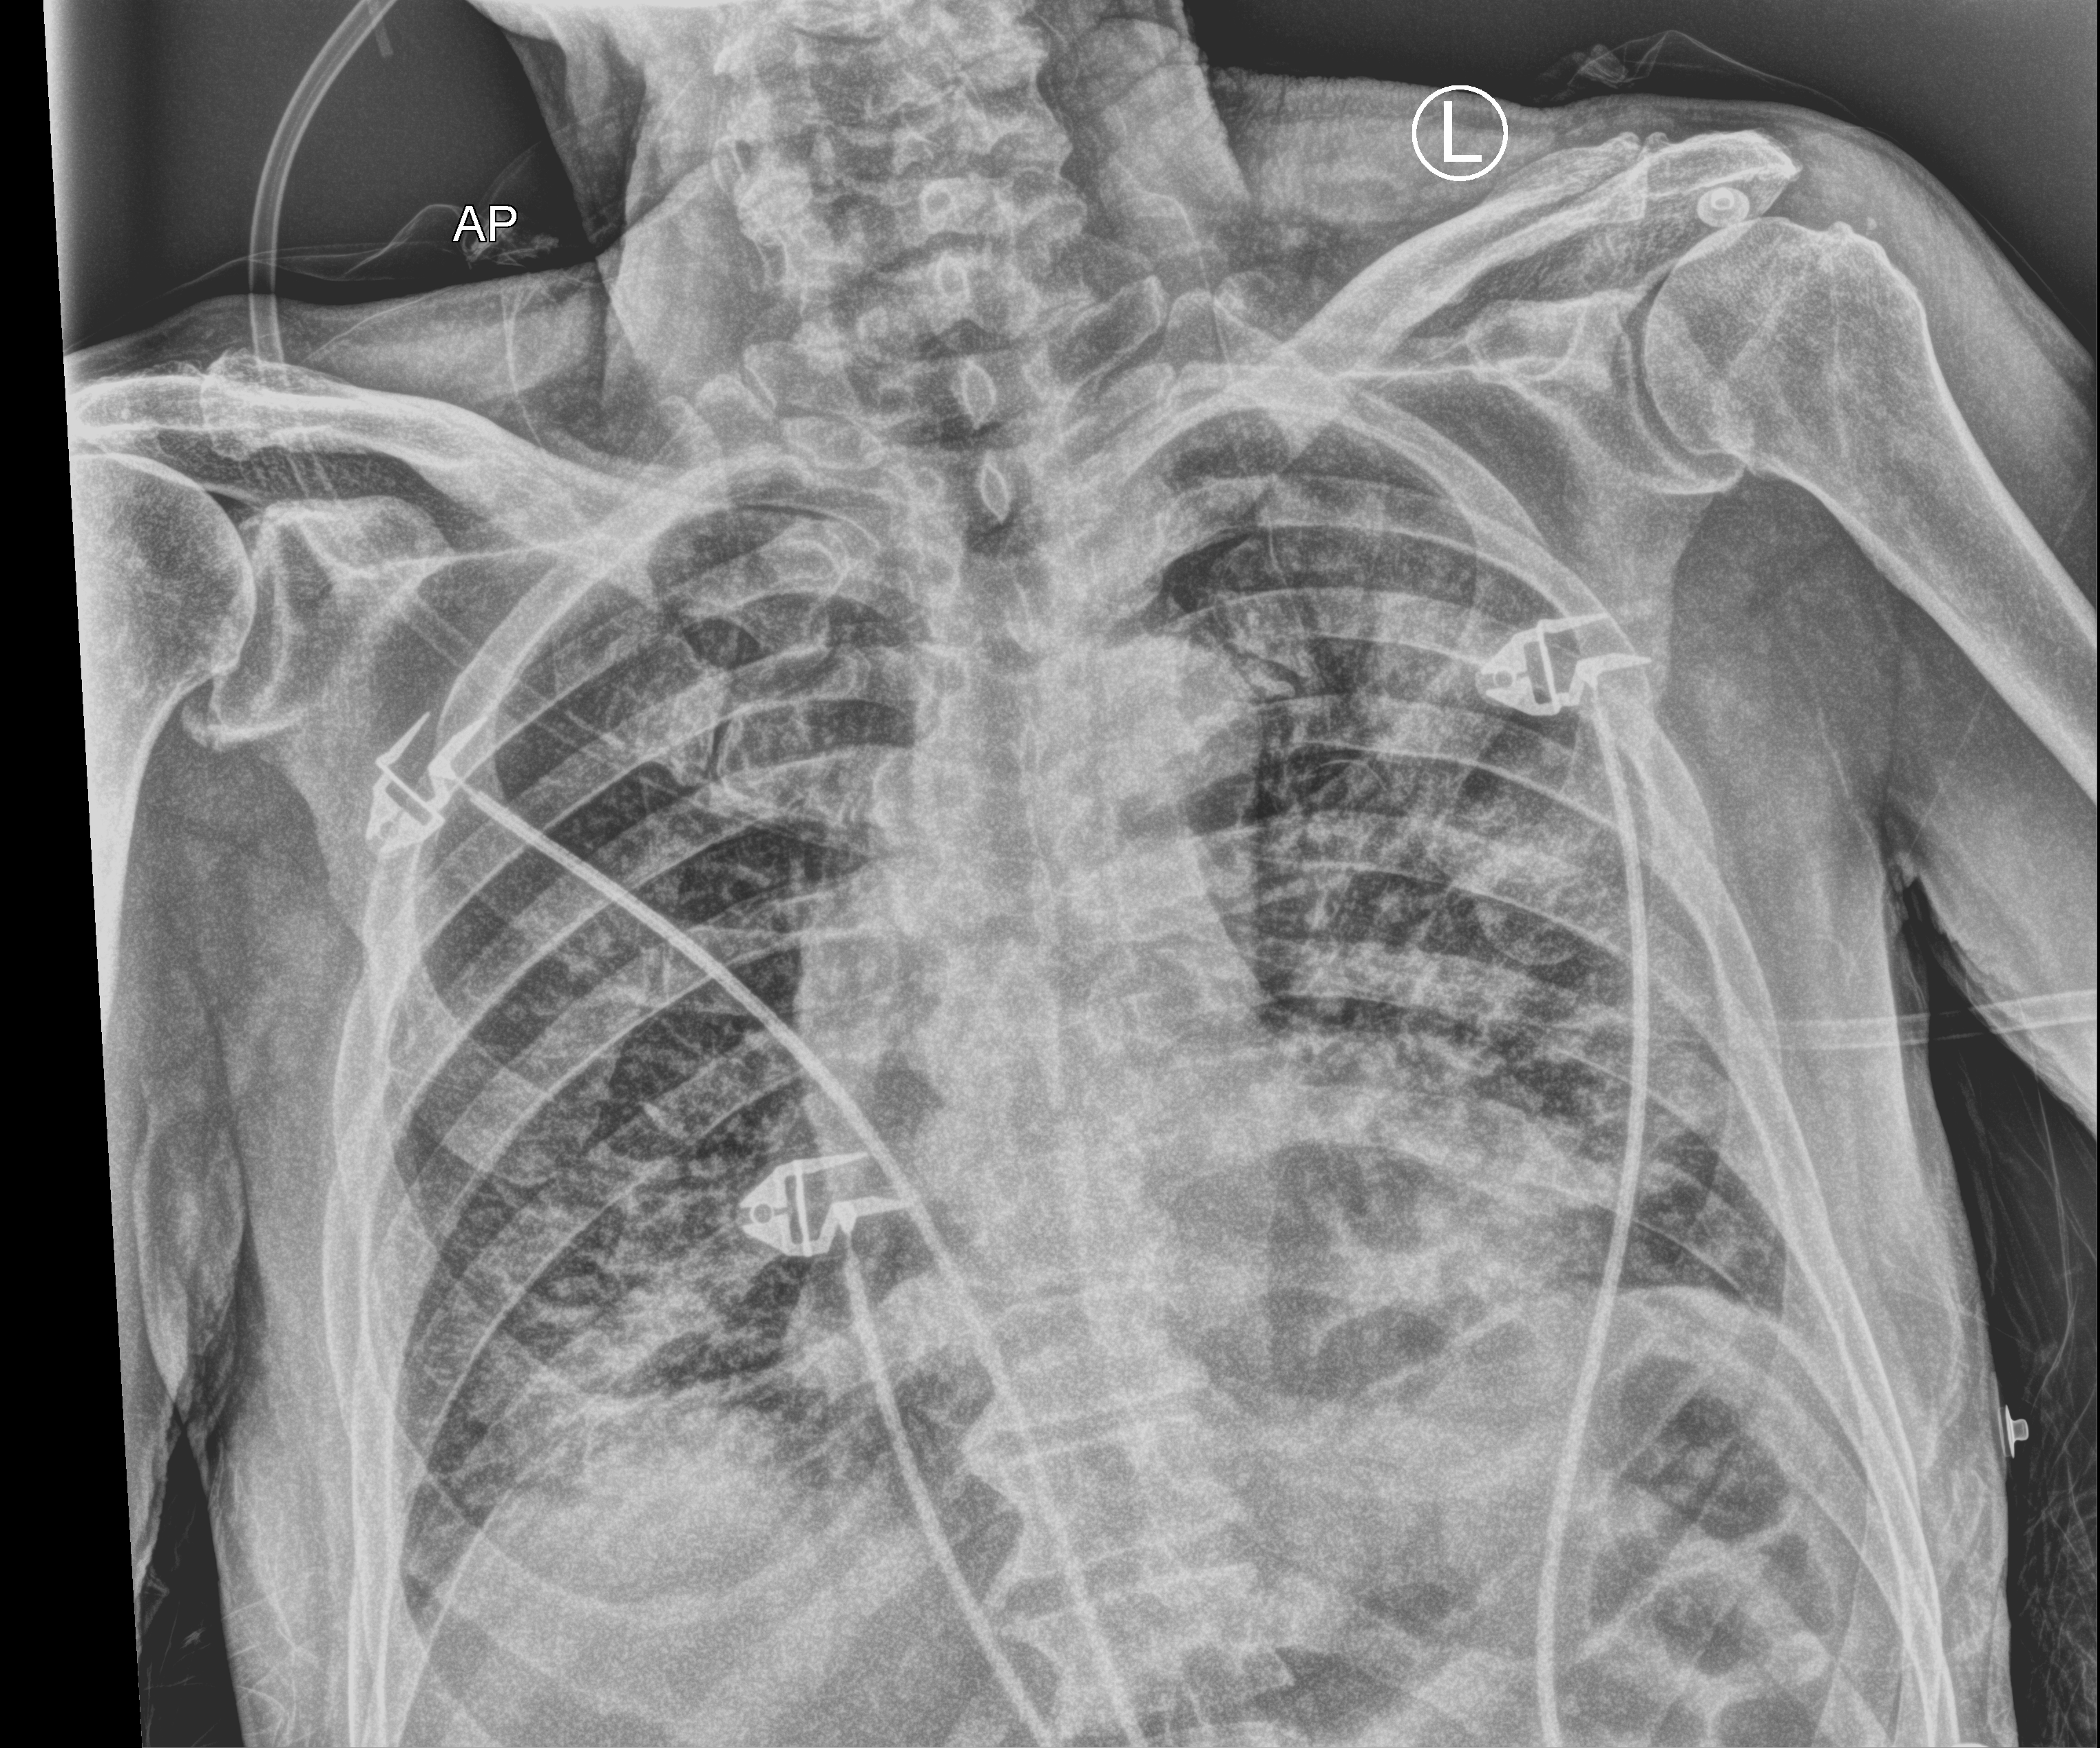
Portable chest radiograph; anteroposterior (AP) projection. Male patient hospitalised with COVID-19, age 75–90 years.
Hospital-stay facts (about this admission, not read from this image; timing relative to this image not recorded):
- length of hospital stay: 17 days
- mechanically ventilated during this hospital stay: no
- admitted to intensive care during this hospital stay: yes